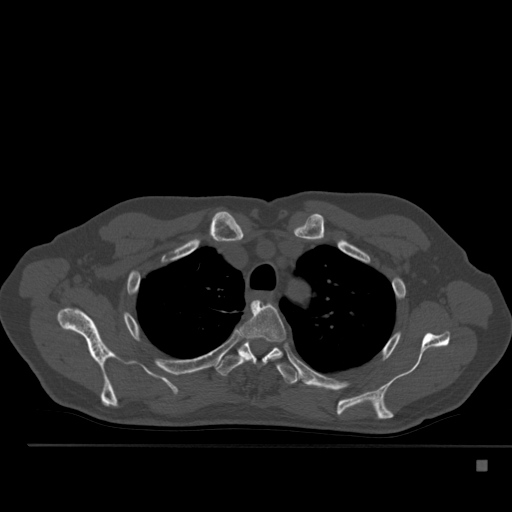
CT including the spine, one axial slice; slice 390 of 517 in the series (ordered by position); reconstruction kernel Br40s; bone window (W 1800 / L 400 HU); 1.5 mm slice thickness; 512 × 512 image matrix, field of view 408 × 408 mm. Male patient, age 70 years. From the clinical record (not read from this slice): primary cancer: renal.
Structures marked on this image (semi-automatically segmented with operator editing):
- T3 vertebra: bounding box <240,300,286,361> (left, top, right, bottom; pixels)
- T4 vertebra: <215,338,300,384>